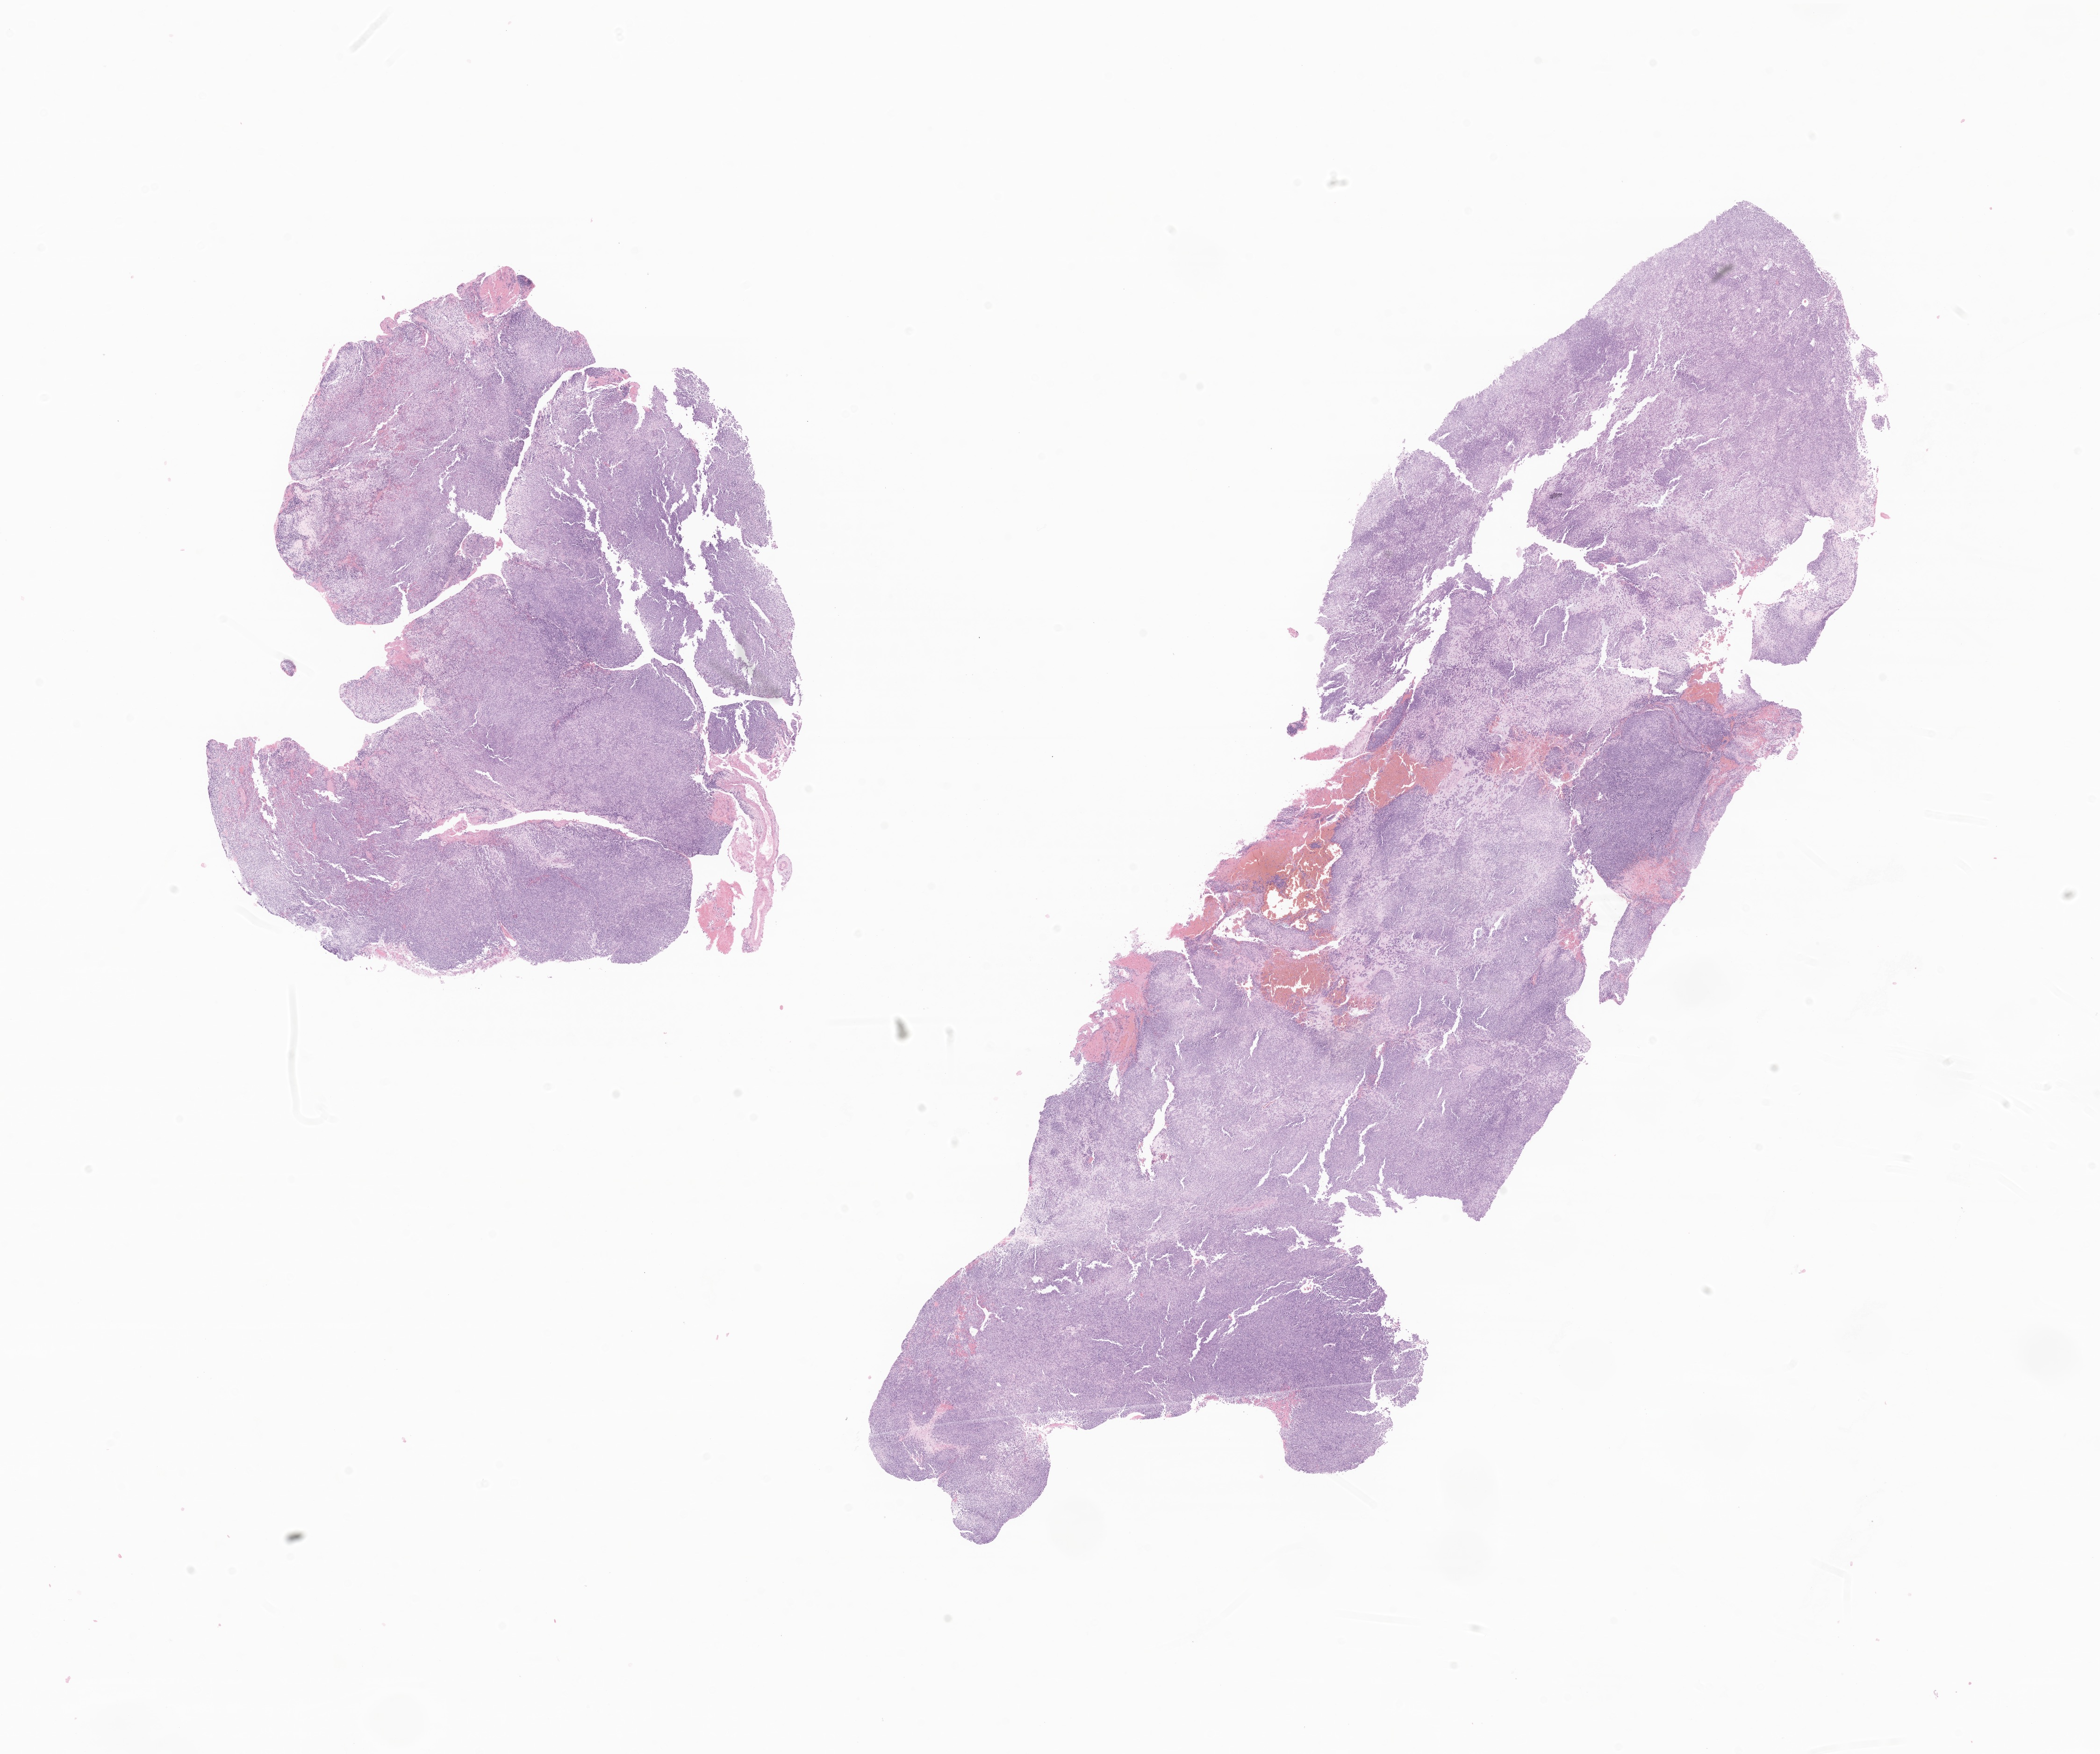
Digitized haematoxylin and eosin-stained section of tumor tissue from the brain — whole scanned area (about 18.9 x 15.8 mm) shown as a low-resolution overview. Formalin-fixed paraffin-embedded section. Female patient, age 603 days (about 1.7 years).
Recorded diagnosis: Neoplasm, malignant.